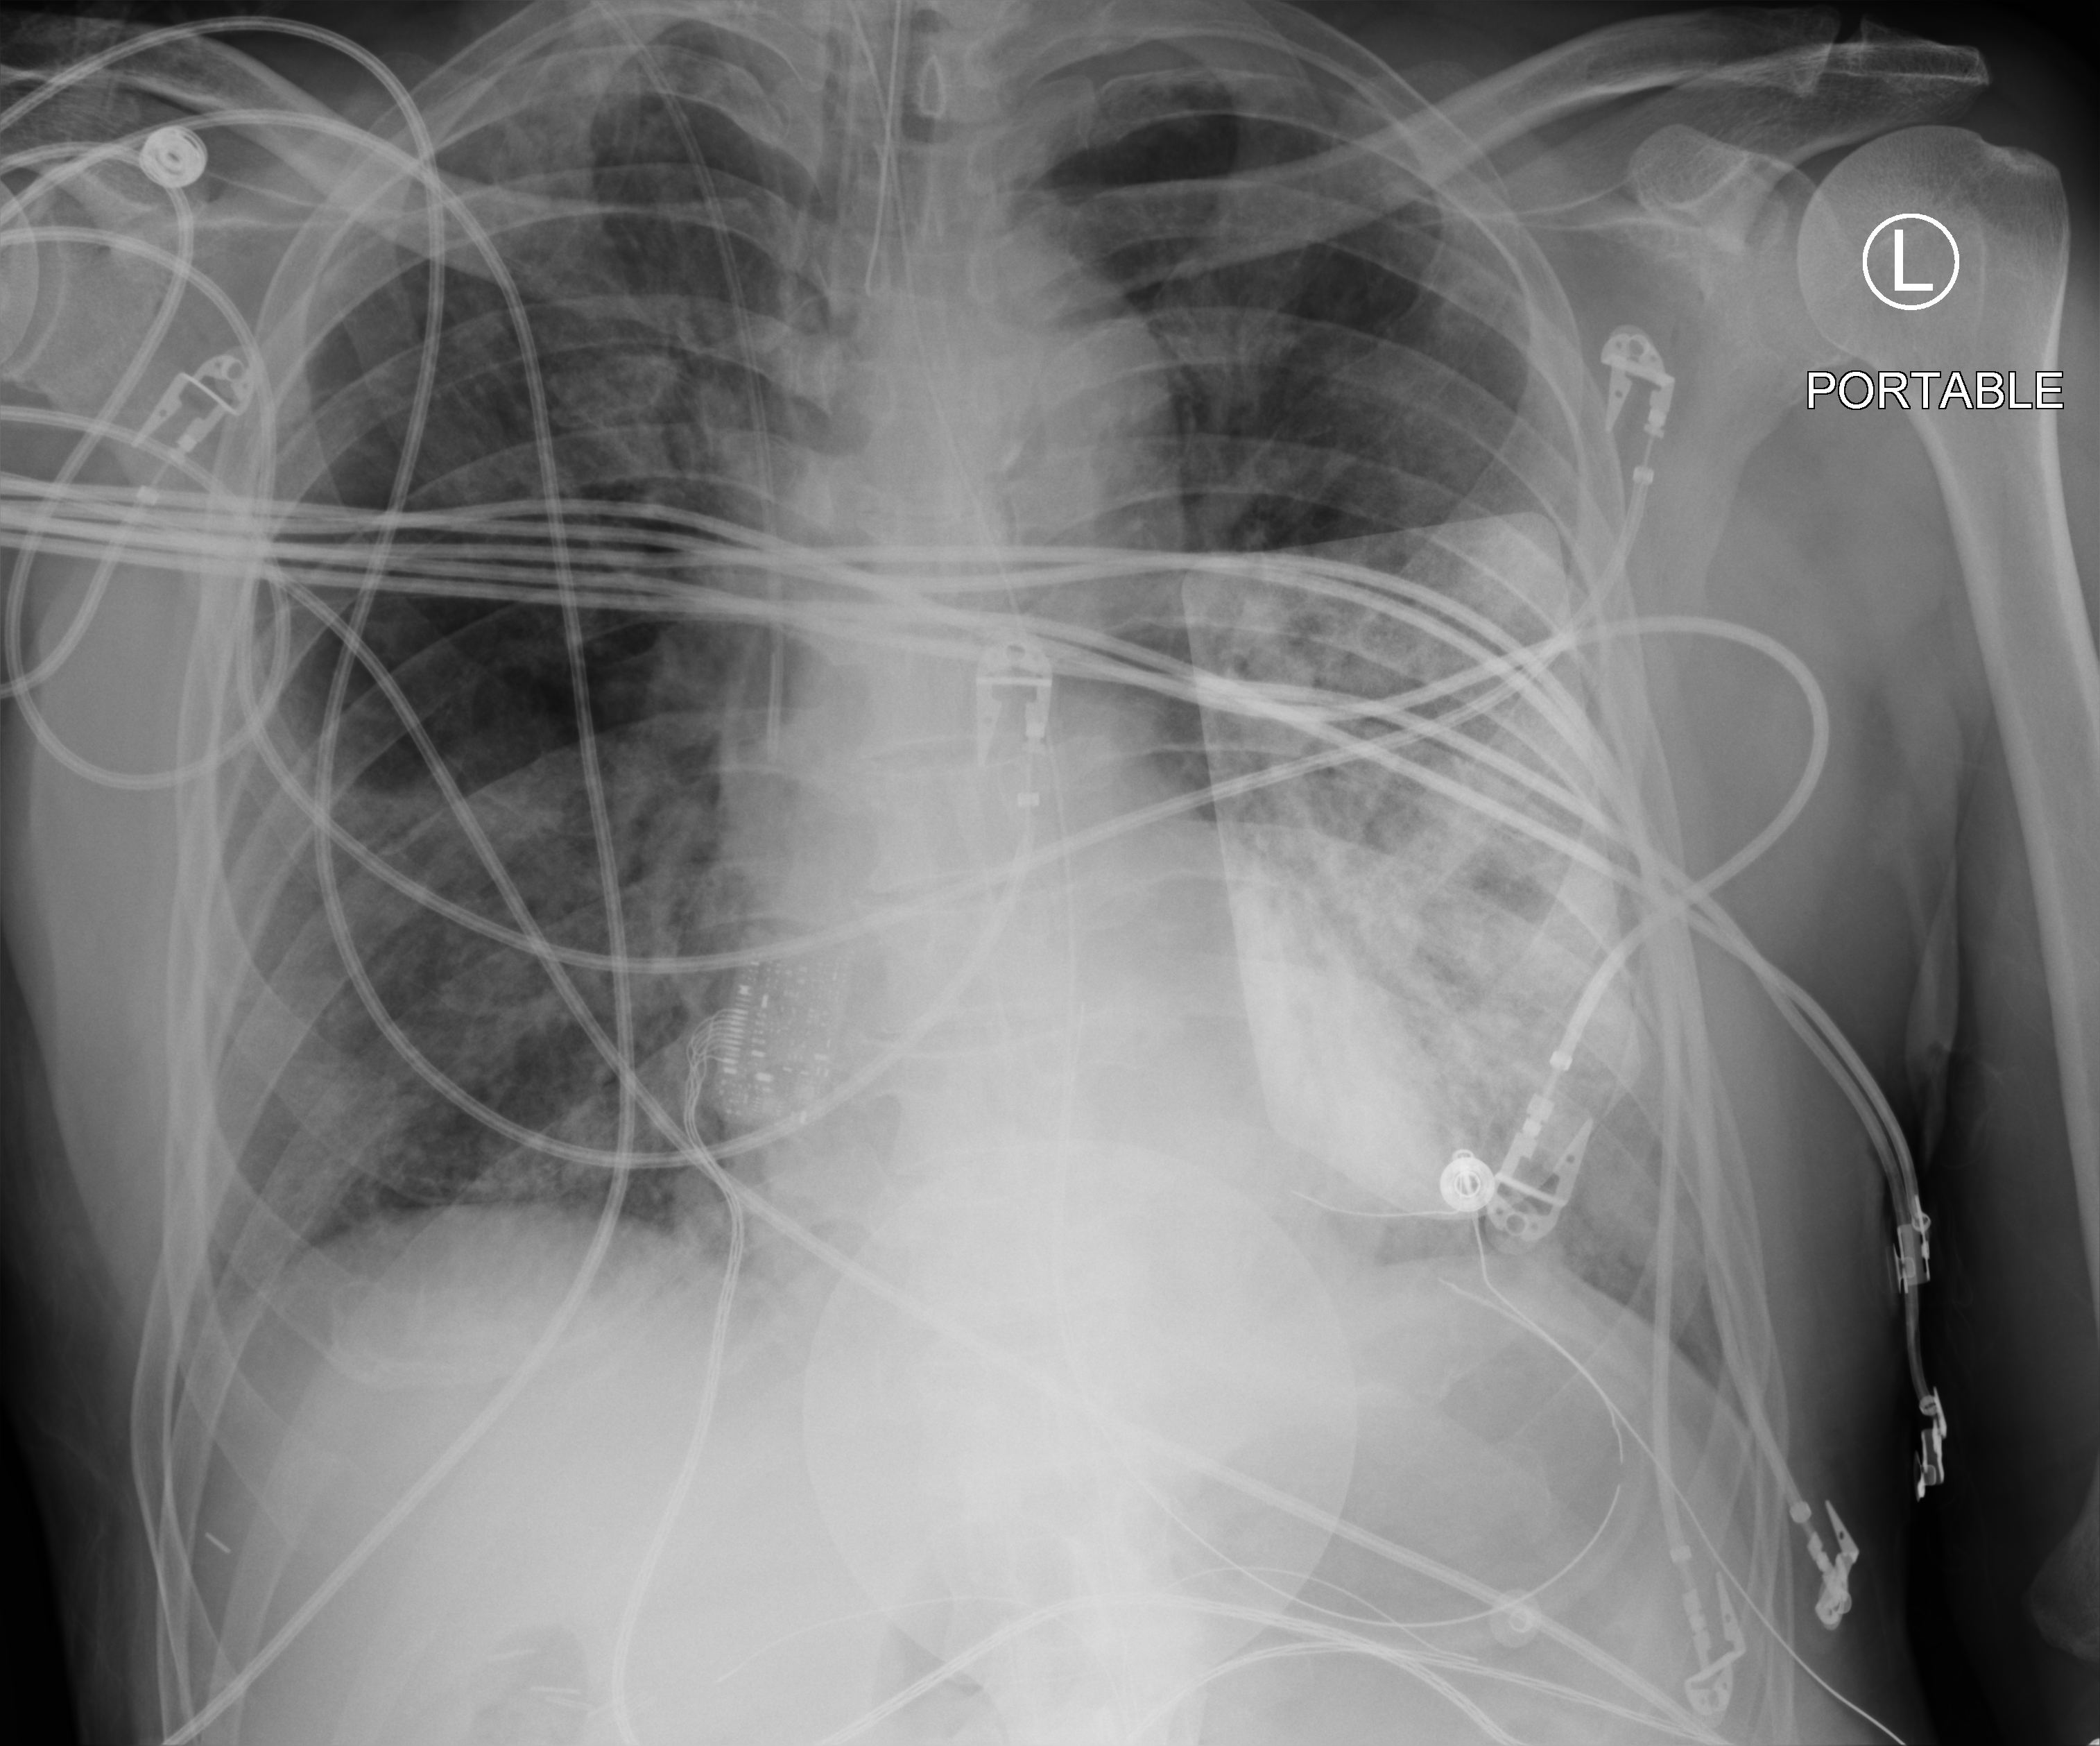
Bedside chest radiograph (computed radiography); anteroposterior (AP) projection. Male patient hospitalised with COVID-19, age 60–74 years.
From the hospital-stay record, not from the radiograph (when in the stay this image was taken is not recorded): COPD (admission record): no.